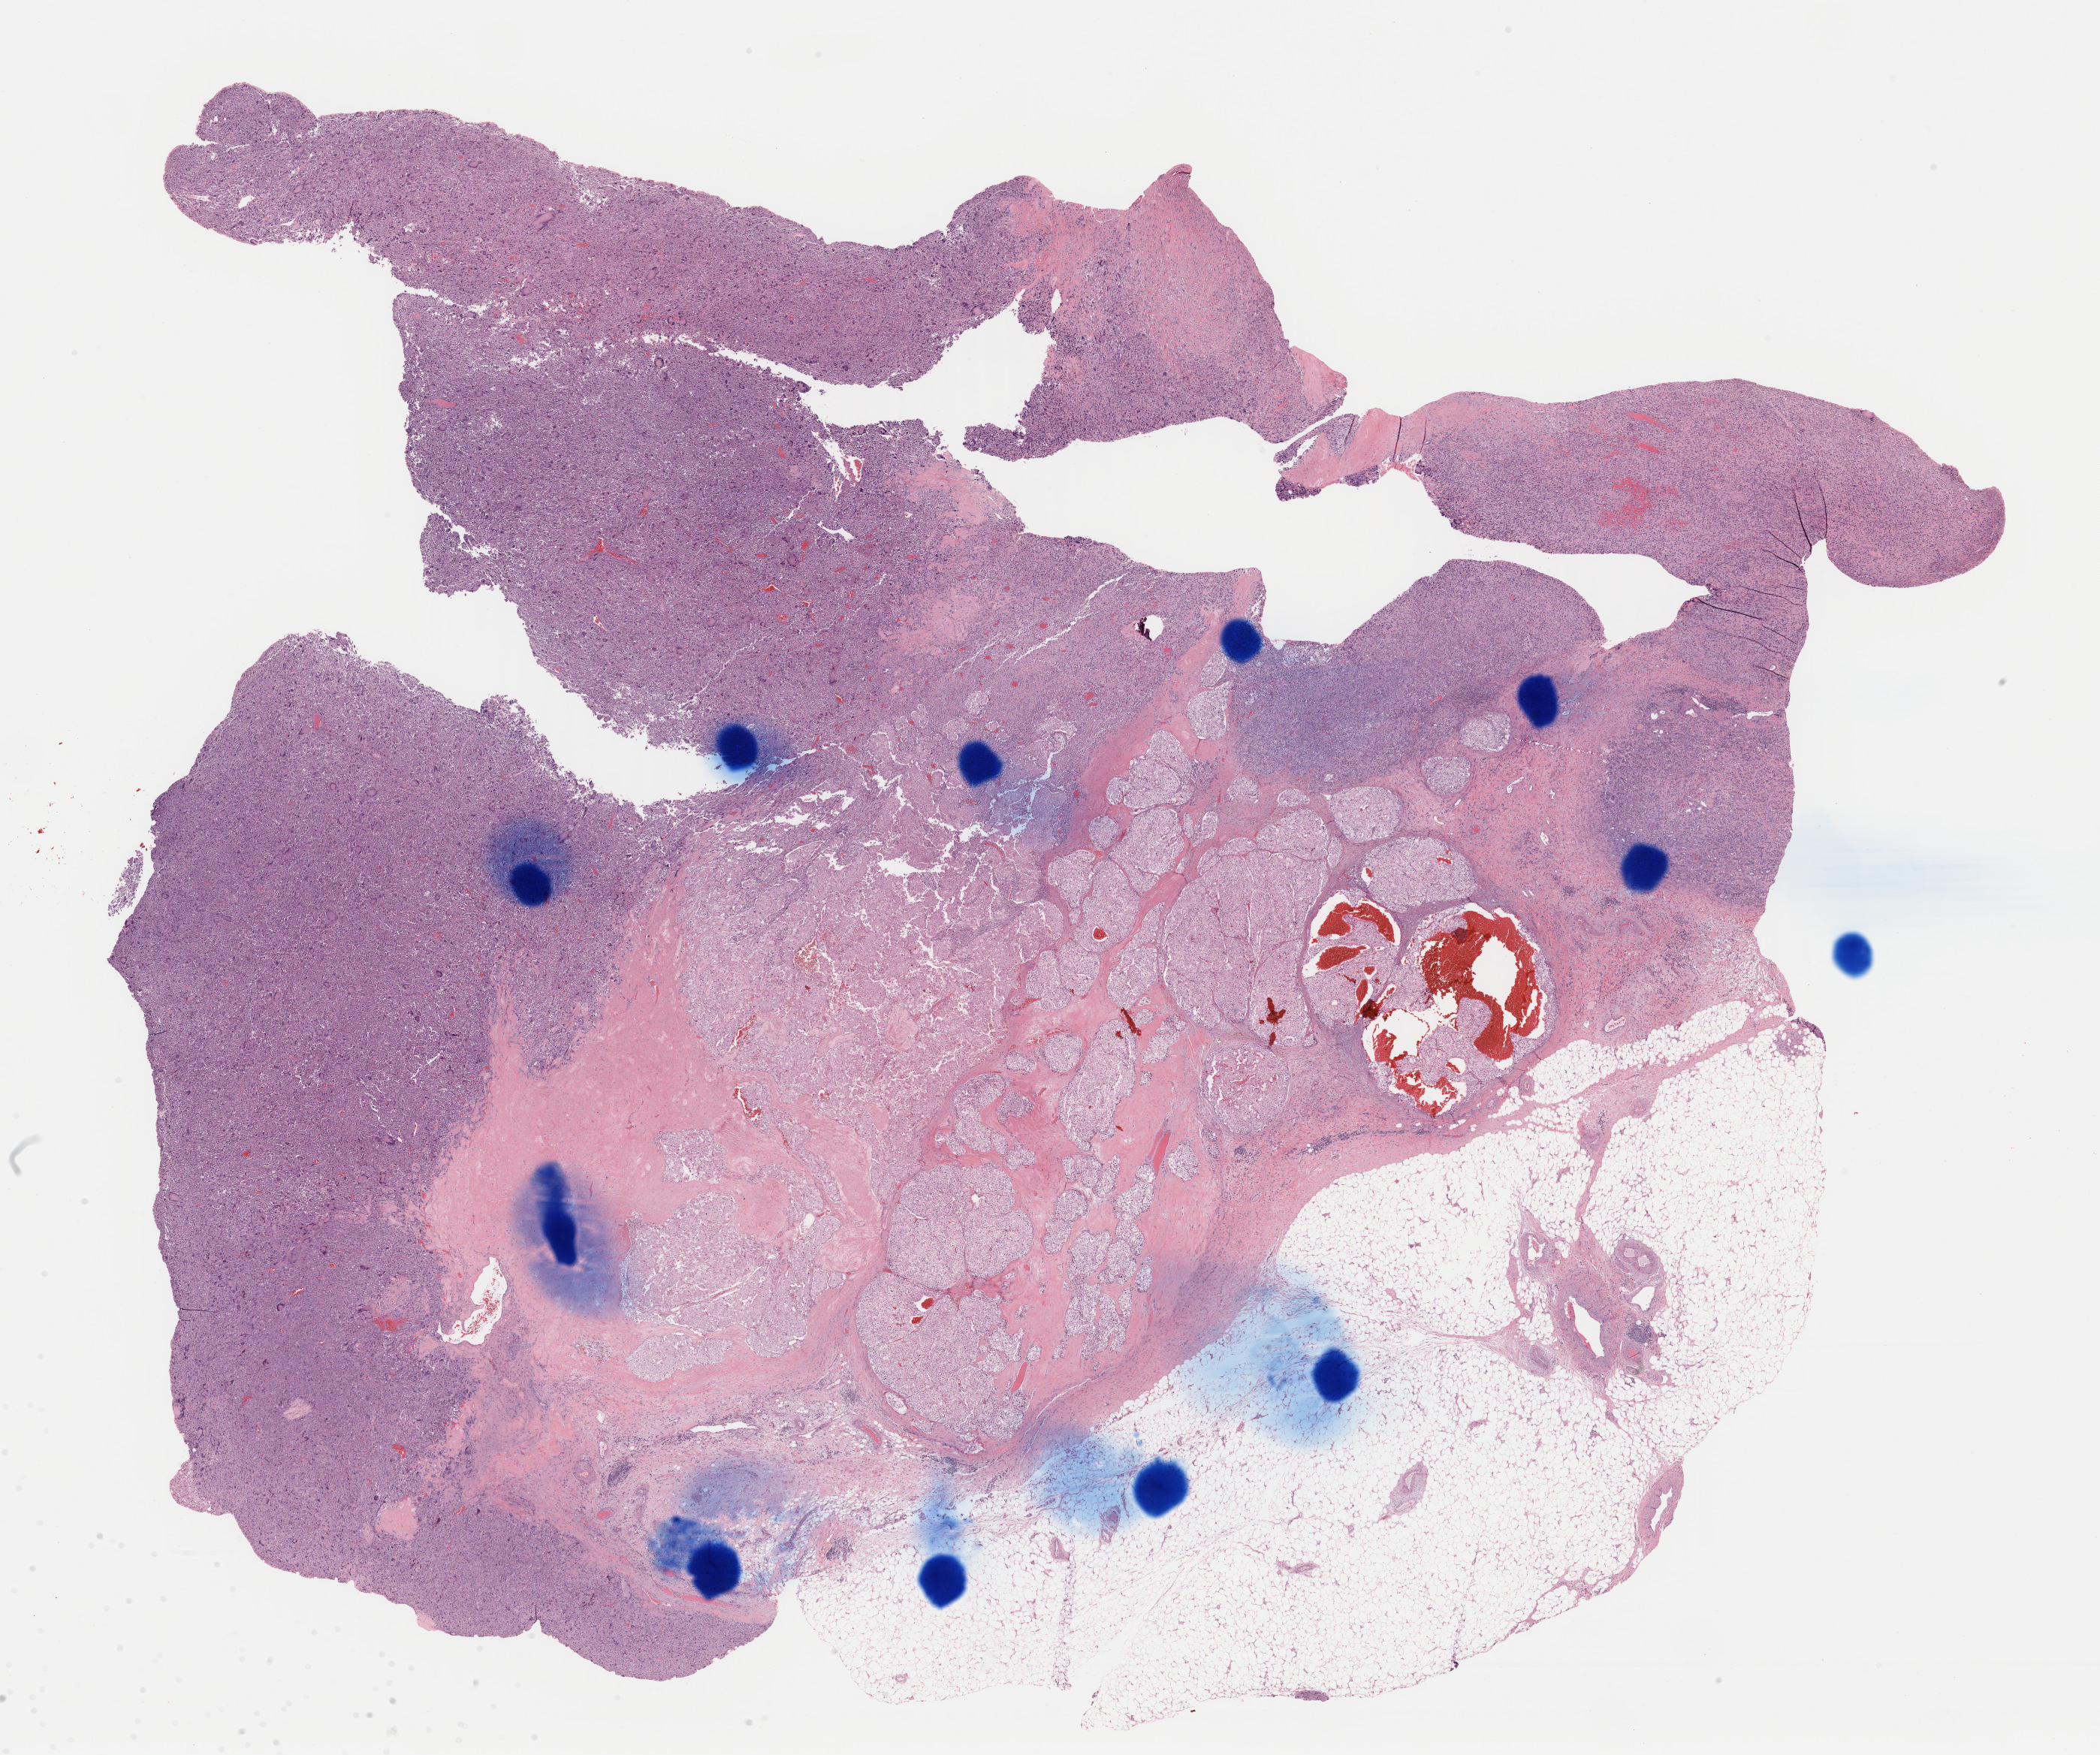
H&E whole-slide image — low-resolution overview of the scanned area, about 22.1 x 18.4 mm (slide scanned at 40x), FFPE section, kidney, primary tumour sample. Male patient; age at initial diagnosis 78 years.
Diagnosis: Renal cell carcinoma, chromophobe type.